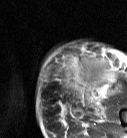
MRI of an extremity soft-tissue mass, one axial slice; slice 18 of 87 in the series (ordered by position); T2-weighted fat-saturated; MR volume resampled by the dataset authors to the PET/CT grid (not the native acquisition matrix); 3.27 mm slice thickness; 127 × 138 image matrix, field of view 124 × 135 mm. Female patient. From the clinical record (not read from this slice): histological type: pleiomorphic leiomyosarcoma; grade: high; site of the primary tumour: left biceps.
Structures marked on this image (expert contour drawn on MRI and transferred to this co-registered scan by the dataset authors):
- gross tumour volume including surrounding oedema: bounding box (x1, y1, x2, y2) in pixels: (59, 55, 119, 104)
- gross tumour volume (mass): (59, 55, 115, 92)